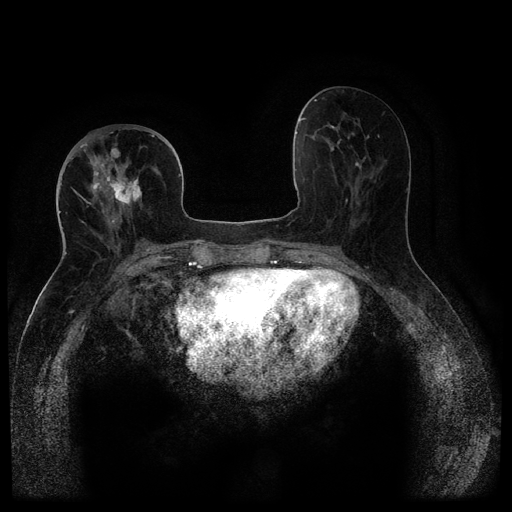
Breast MRI (dynamic contrast-enhanced, multi-phase), one axial slice; position 46 of 116 along the scan axis; dynamic contrast-enhanced series, time point 2 of 5 at this slice position (early post-contrast); 1.5 T; TE 2.6 ms, TR 5.4 ms; 512 × 512 image matrix. Patient: female, 68 years.
Annotated regions visible in this slice (semi-automatic segmentation, software-assisted and operator-edited):
- breast lesion (labelled 'tumour' in the annotation; benign lesions carry a separate 'benign' label): bounding box <106,171,143,210> (left, top, right, bottom; pixels)